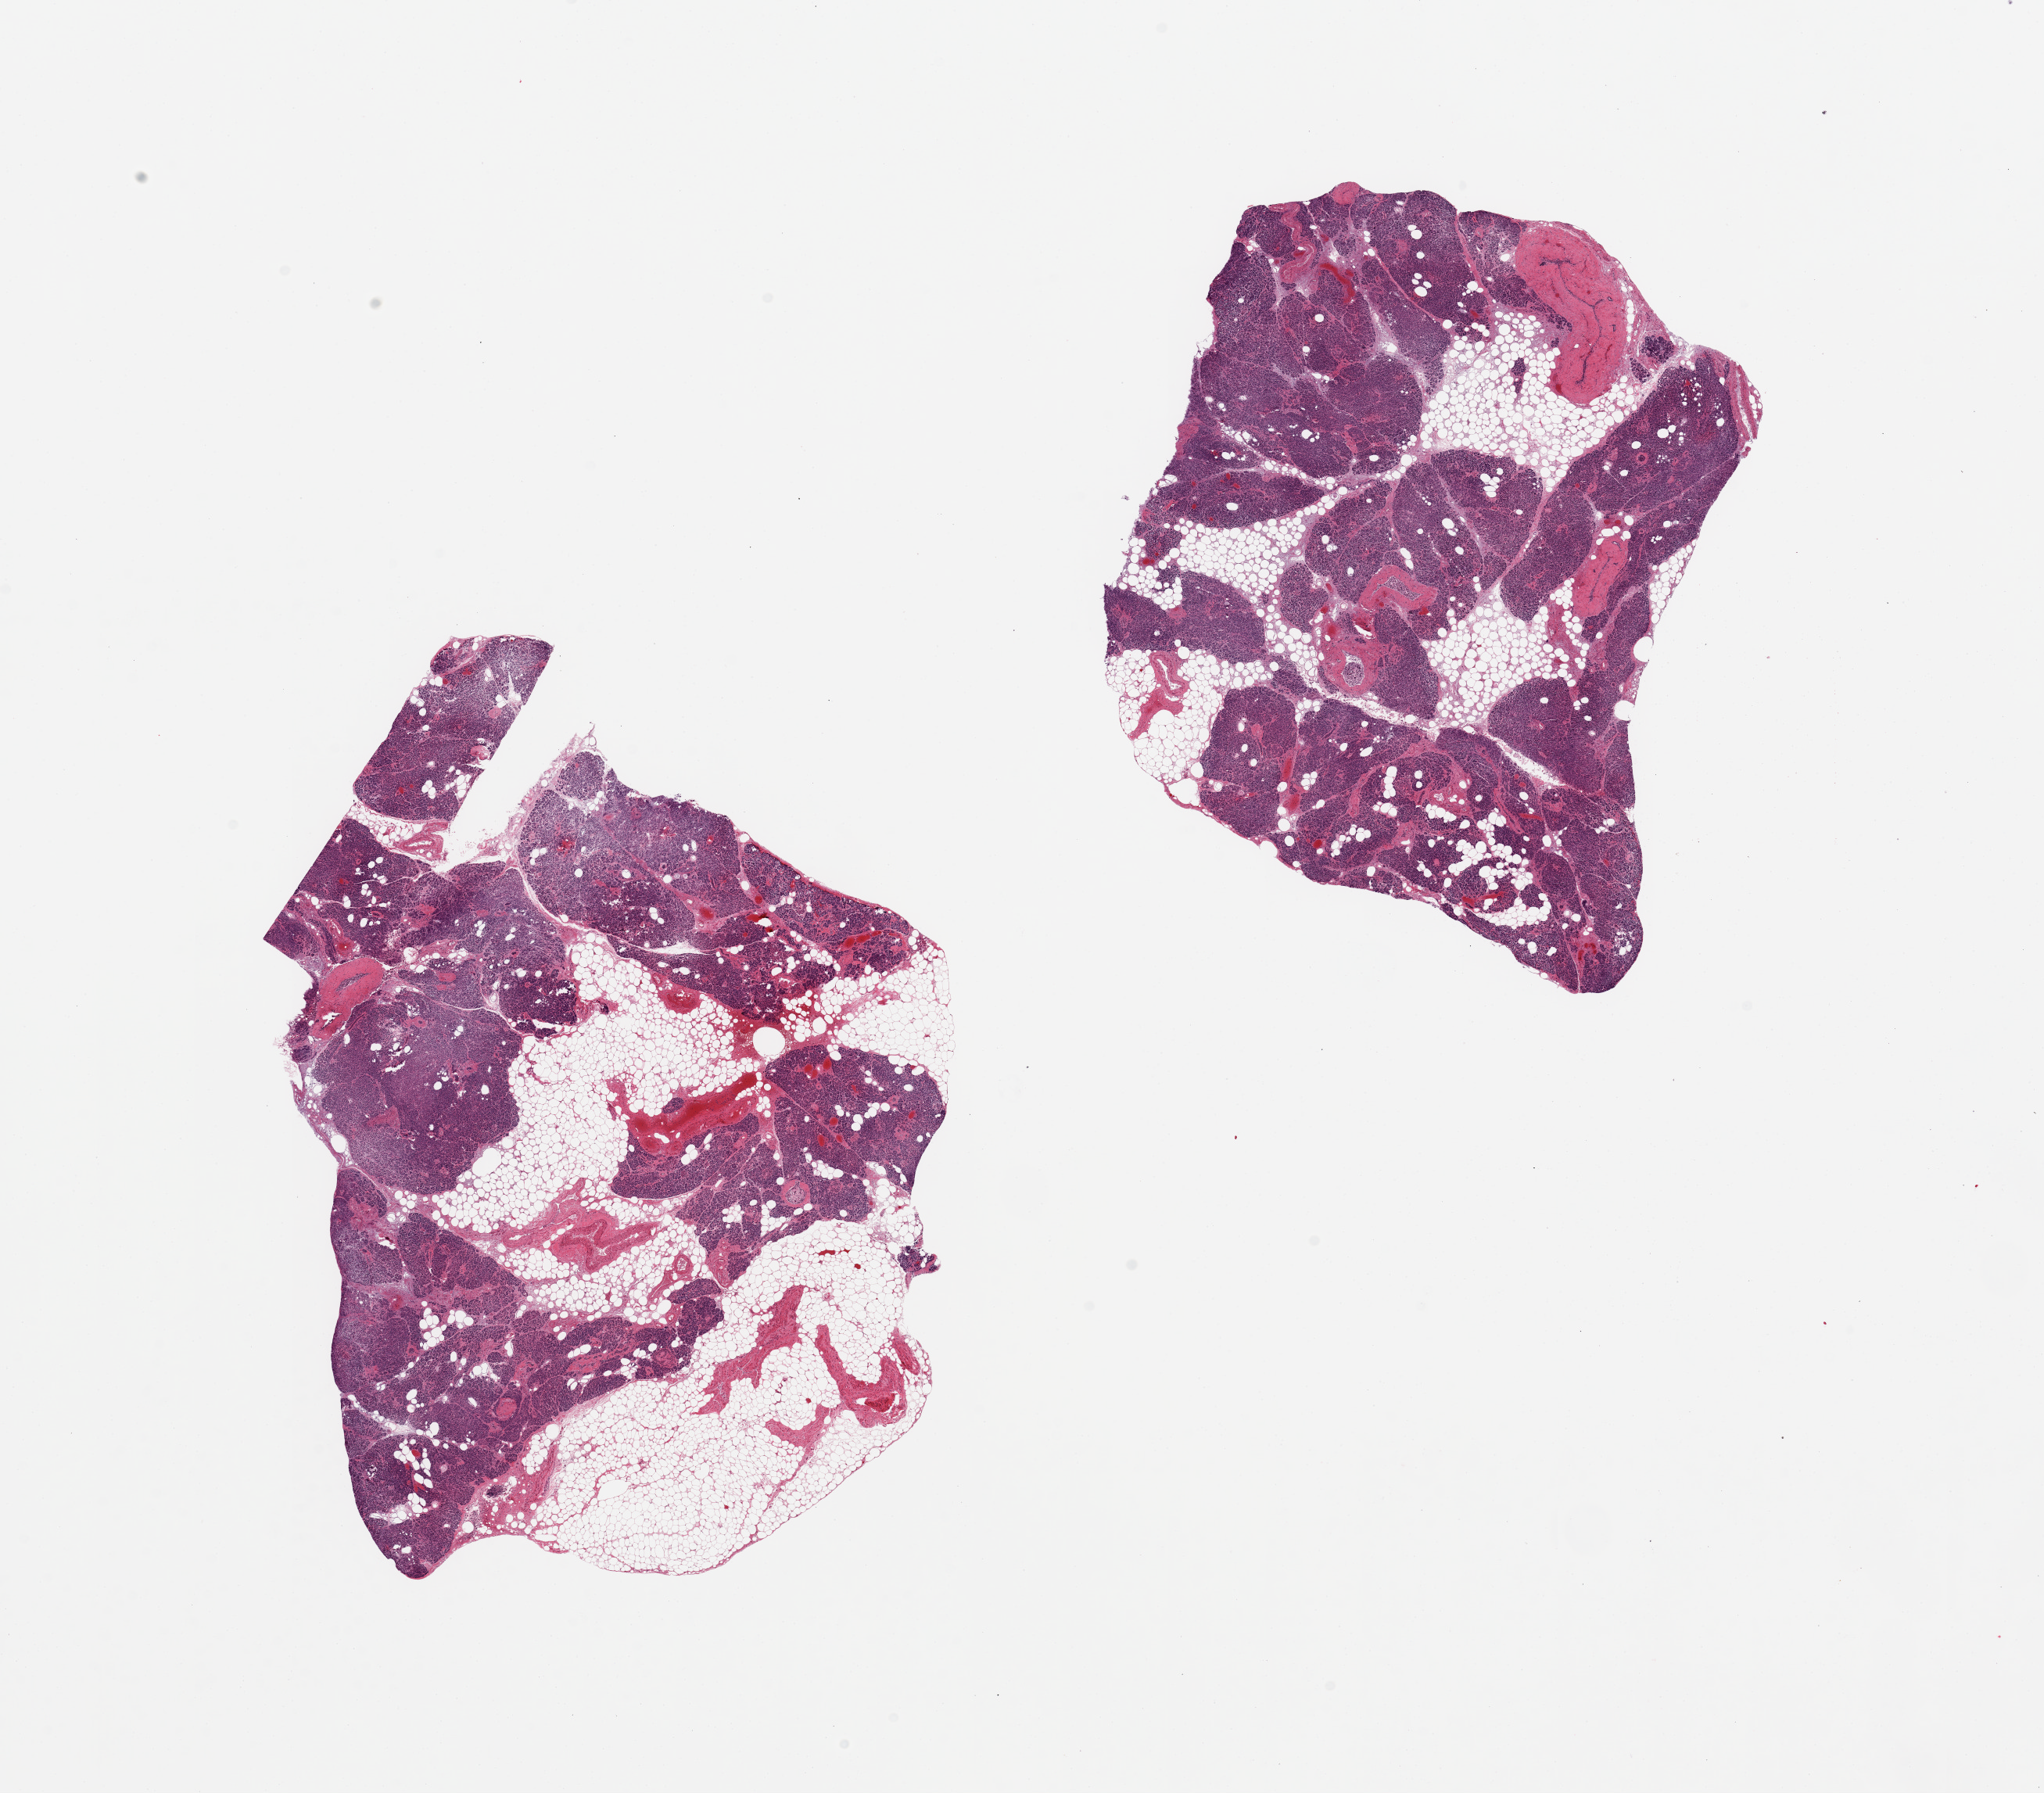
Digitized H&E-stained section, brightfield — a low-resolution overview of the entire scanned area, about 20.7 x 18.1 mm, PAXgene-fixed, paraffin-embedded tissue, section of pancreas (target tissue), tissue donor sample. Donor sex: female.
Pathologist's review note for this sample: 2 pieces; 40 & 50% internal & external fat.